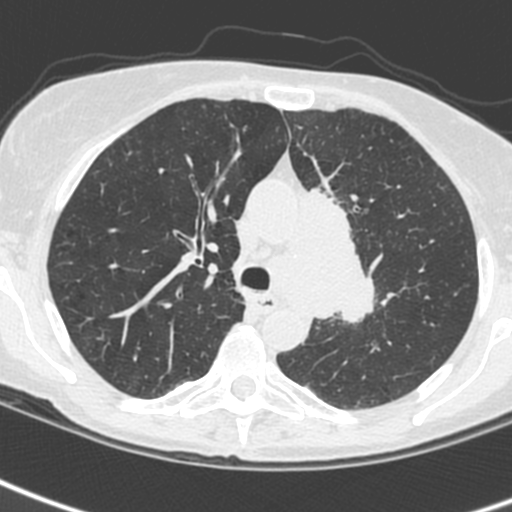
Low-dose screening chest CT, one axial slice. Position 169 of 242 along the scan axis. Lung window (W 1500 / L -600 HU). 512 × 512 image matrix, field of view 284 × 284 mm.
Structures marked on this image (expert manual segmentation):
- lesion 3 (tumor, upper lobe of left lung): bounding box <305,188,376,324> (left, top, right, bottom; pixels)